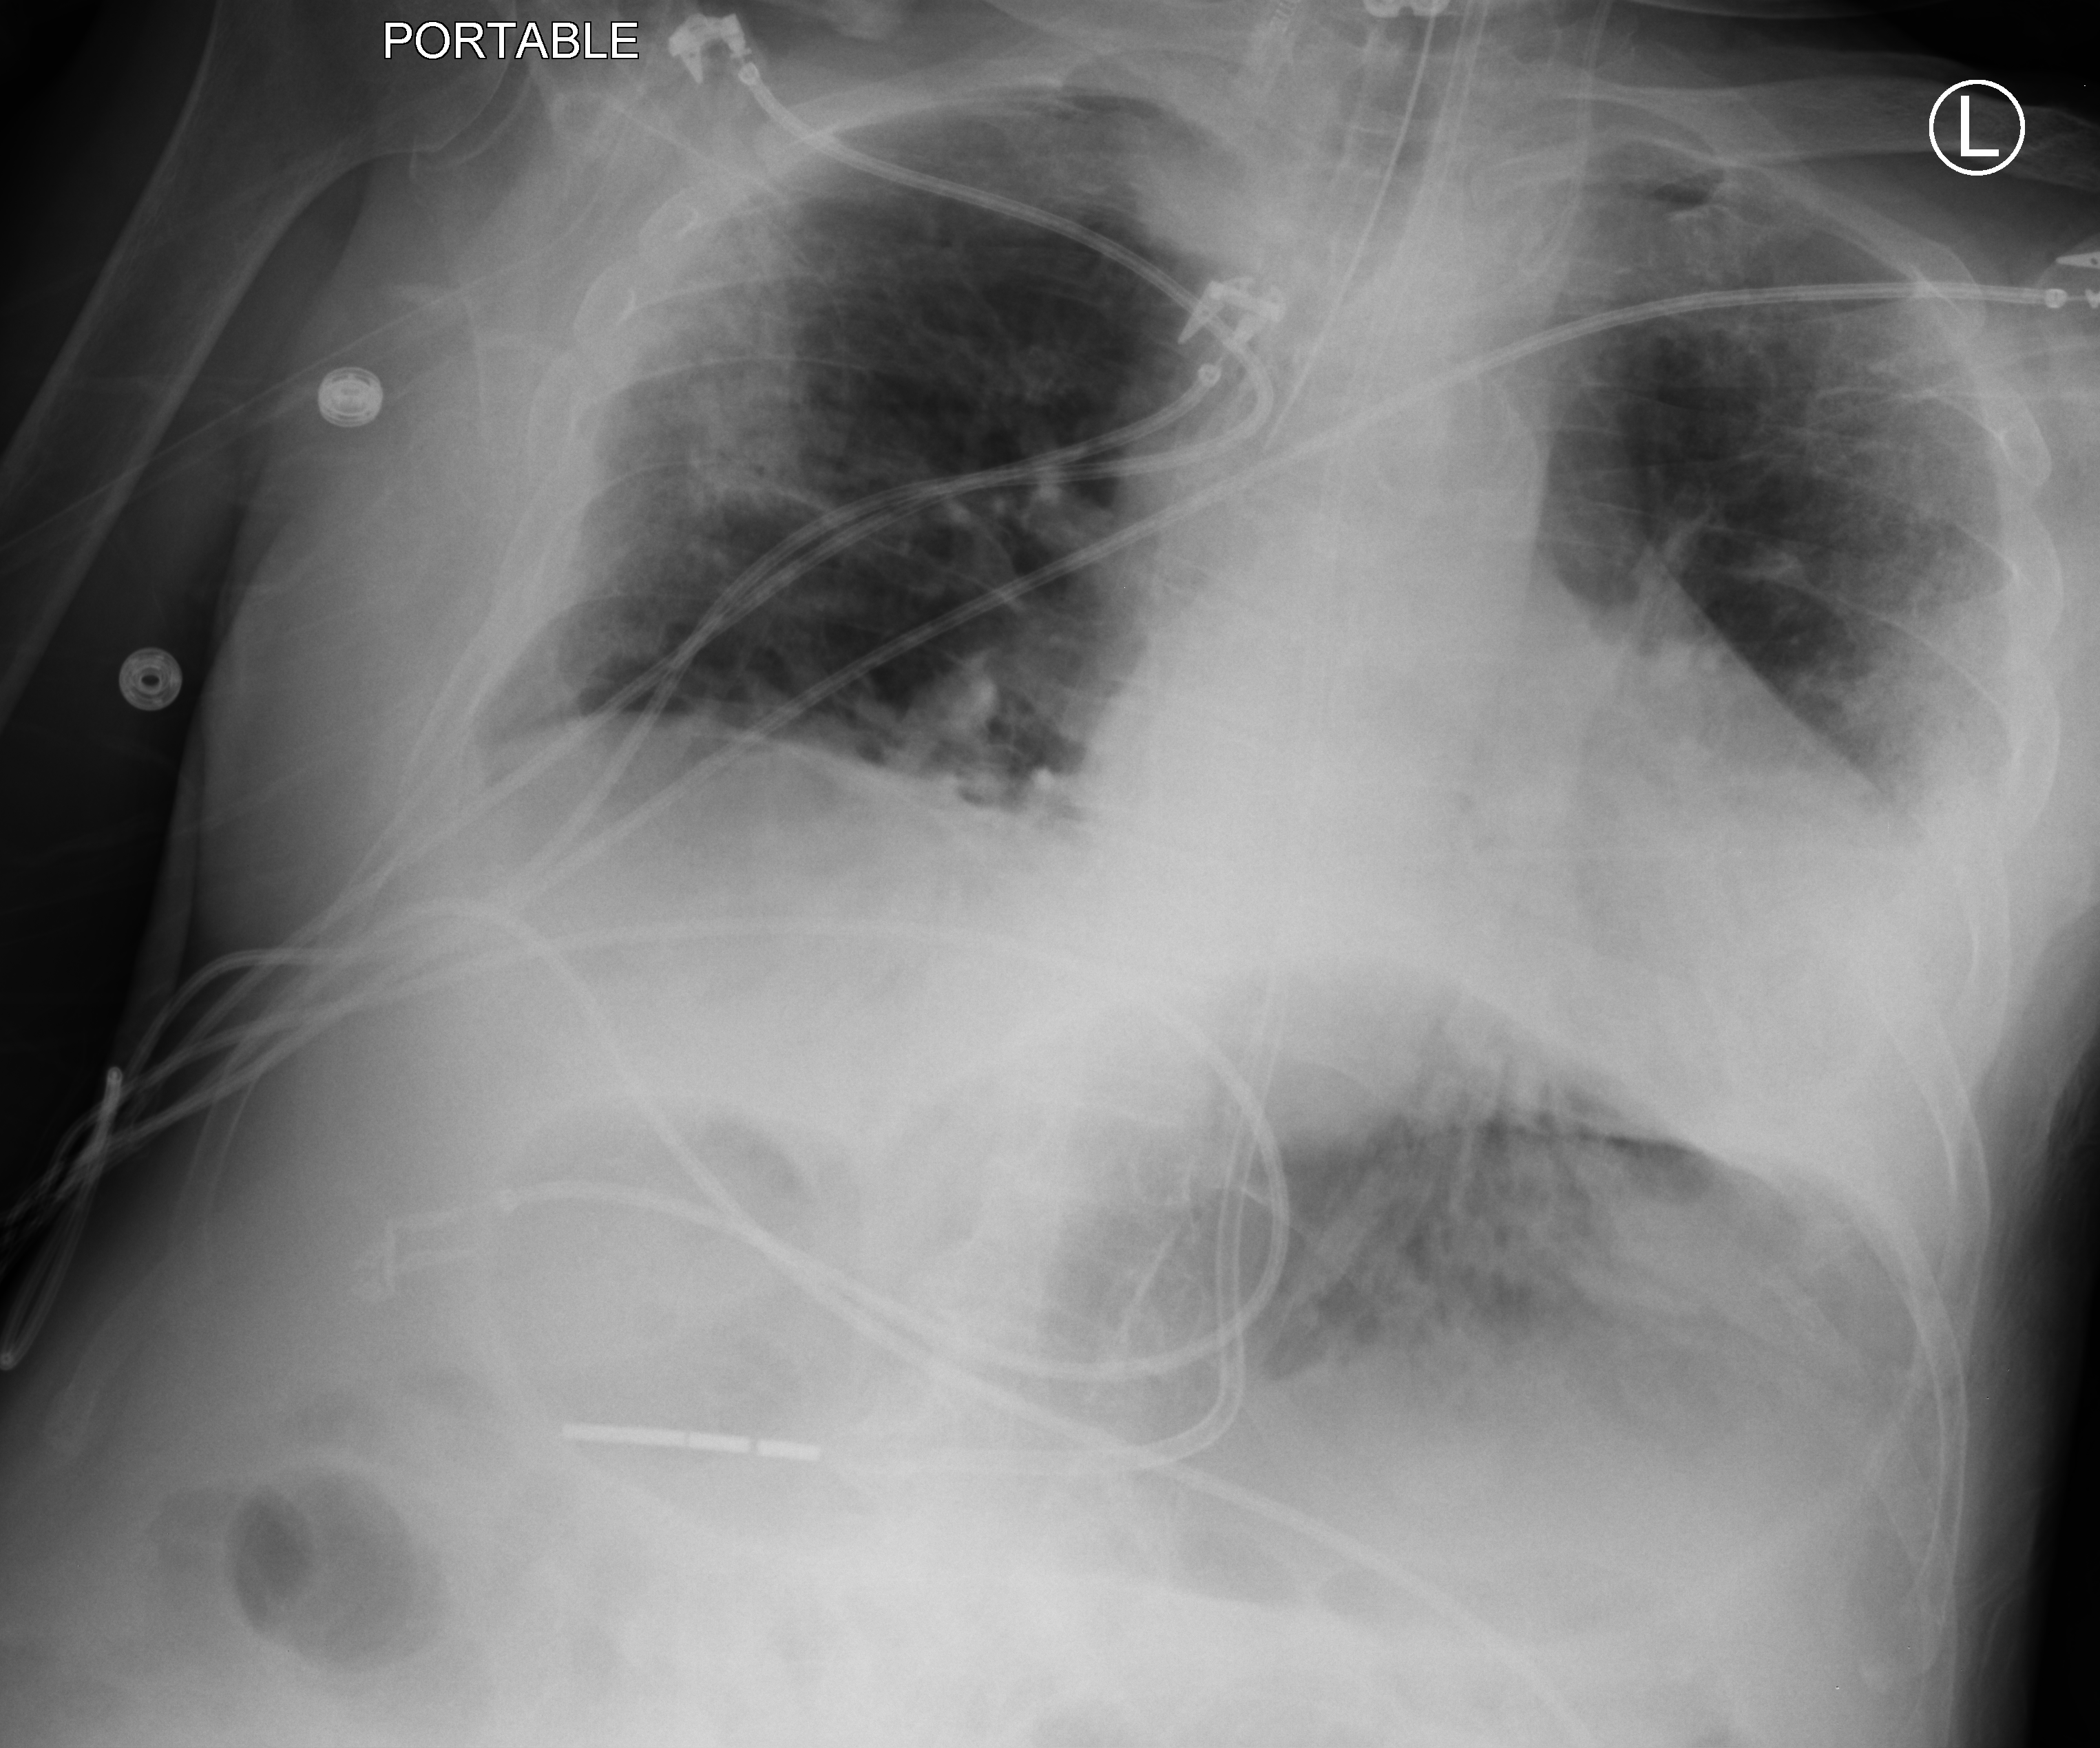
Chest X-ray (portable), anteroposterior (AP) projection. Patient hospitalised with COVID-19; male, aged 75–90 years.
Admission-level facts for this patient (not findings on this image; timing relative to this image not recorded): mechanically ventilated during this hospital stay: yes; admitted to intensive care during this hospital stay: yes.